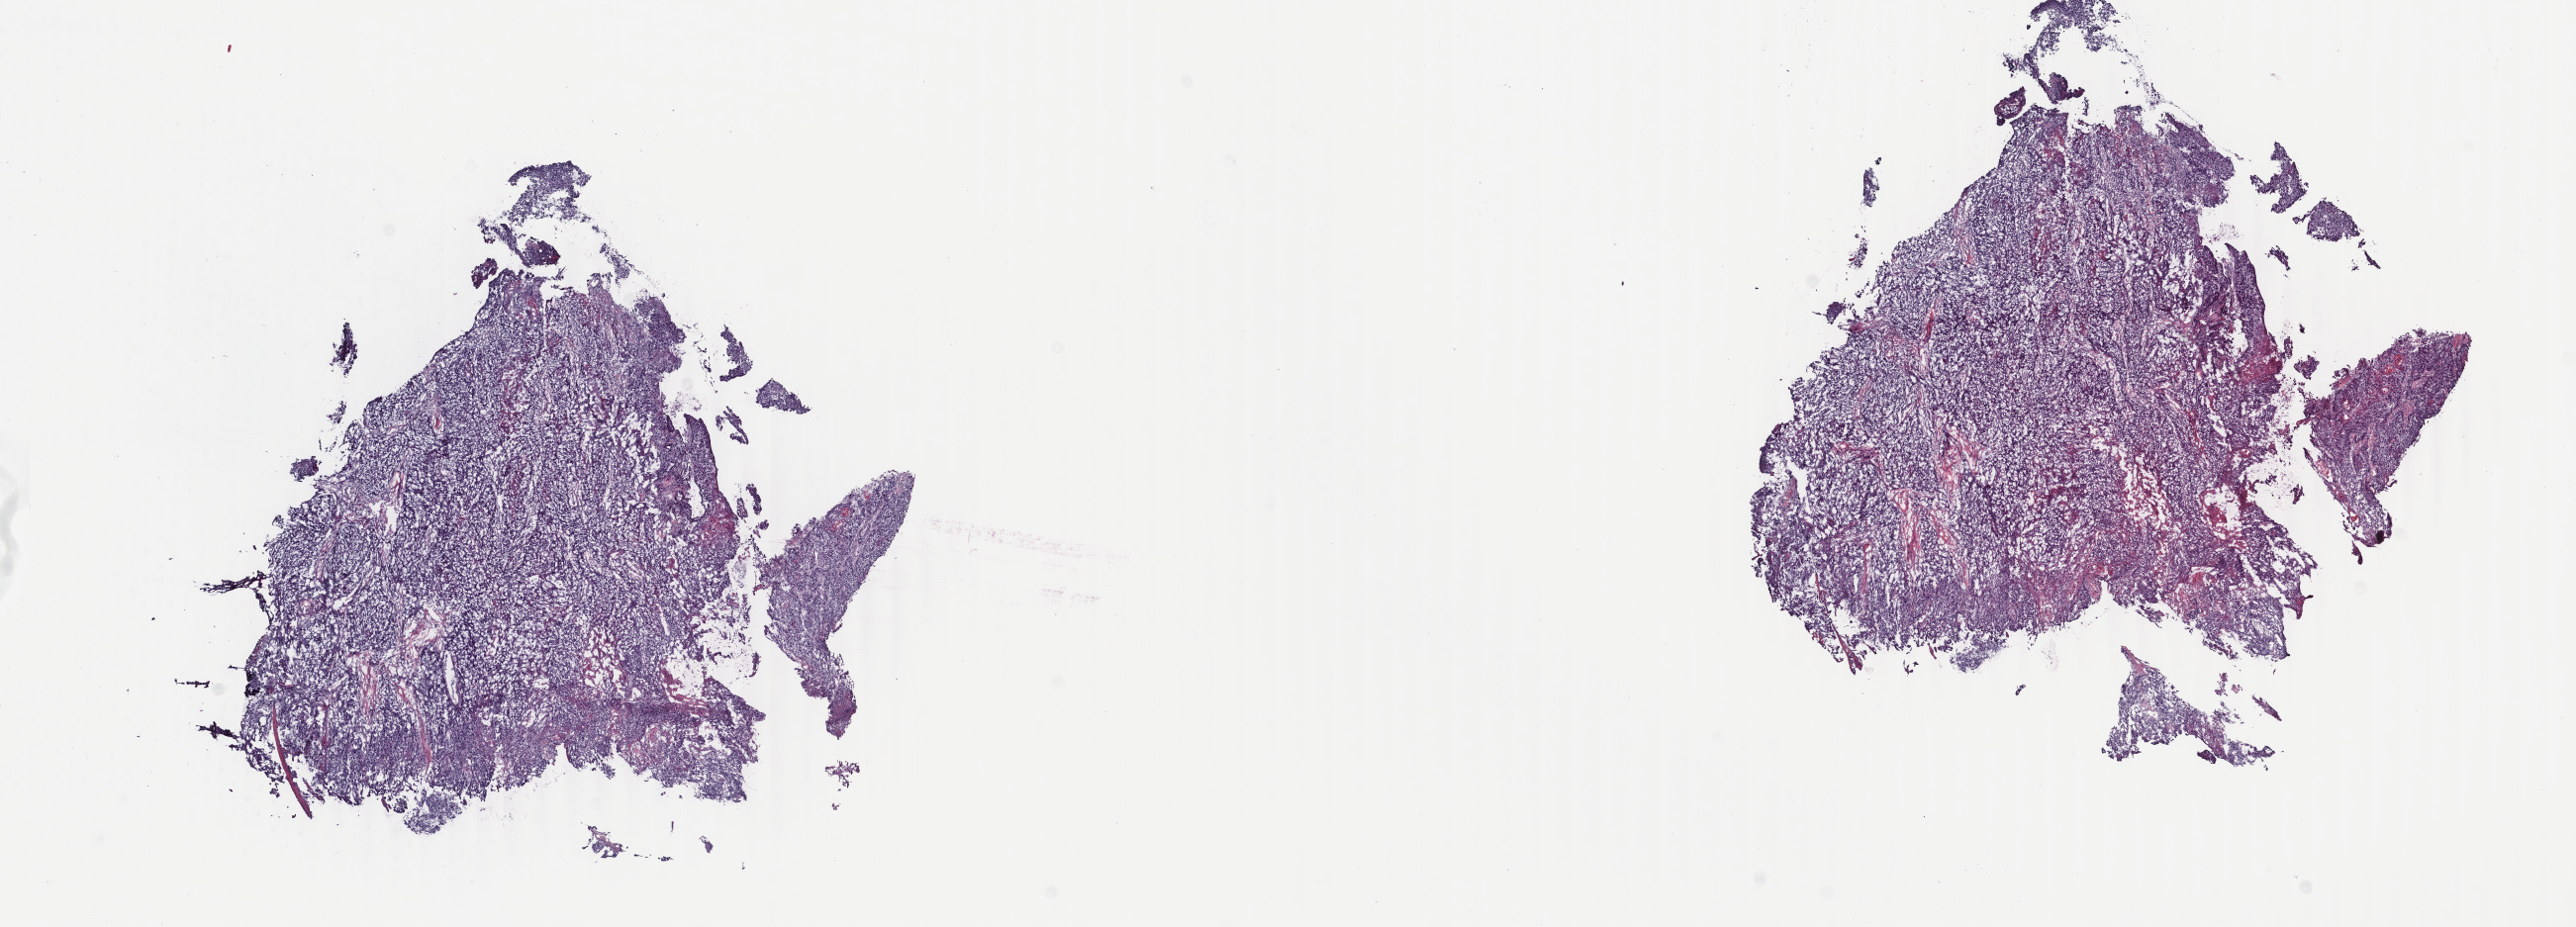
Whole-slide histology image, Hematoxylin and eosin (H&E) stained, whole scanned area (about 20.7 x 7.5 mm, slide scanned at 40x) shown as a low-resolution overview; frozen section; primary tumour sample from the head and neck. Patient: male, age at initial diagnosis 71 years. Histologic grade: G3 (poorly differentiated). Pathologist review of this section (percent, as recorded): tumour cells 95%, tumour nuclei 99%, normal cells 0%, stromal cells 5%, necrosis 0%. Inflammatory infiltration, as recorded: lymphocyte infiltration 0%, monocyte infiltration 0%, neutrophil infiltration 0%.
Histologic diagnosis: Squamous cell carcinoma, NOS. AJCC pathologic stage: III (7th edition).